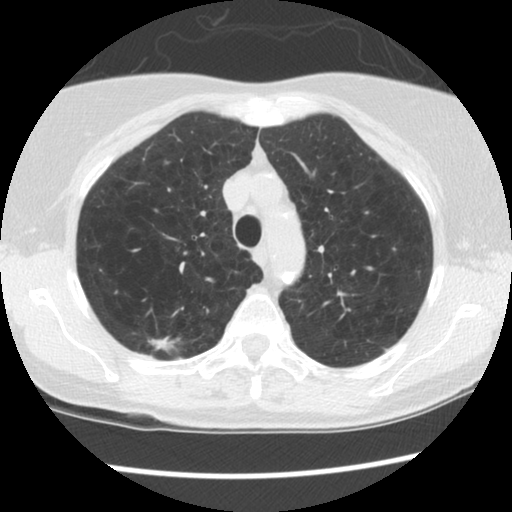
Low-dose screening chest CT, one axial slice. Position 104 of 134 along the scan axis. Lung window (W 1500 / L -600 HU). 2.5 mm slice thickness. 512 × 512 image matrix.
Annotated regions visible in this slice (outlined manually by an expert reader):
- lesion 1 (tumor, upper lobe of right lung): bounding box [x1, y1, x2, y2] px = [148, 336, 180, 356]